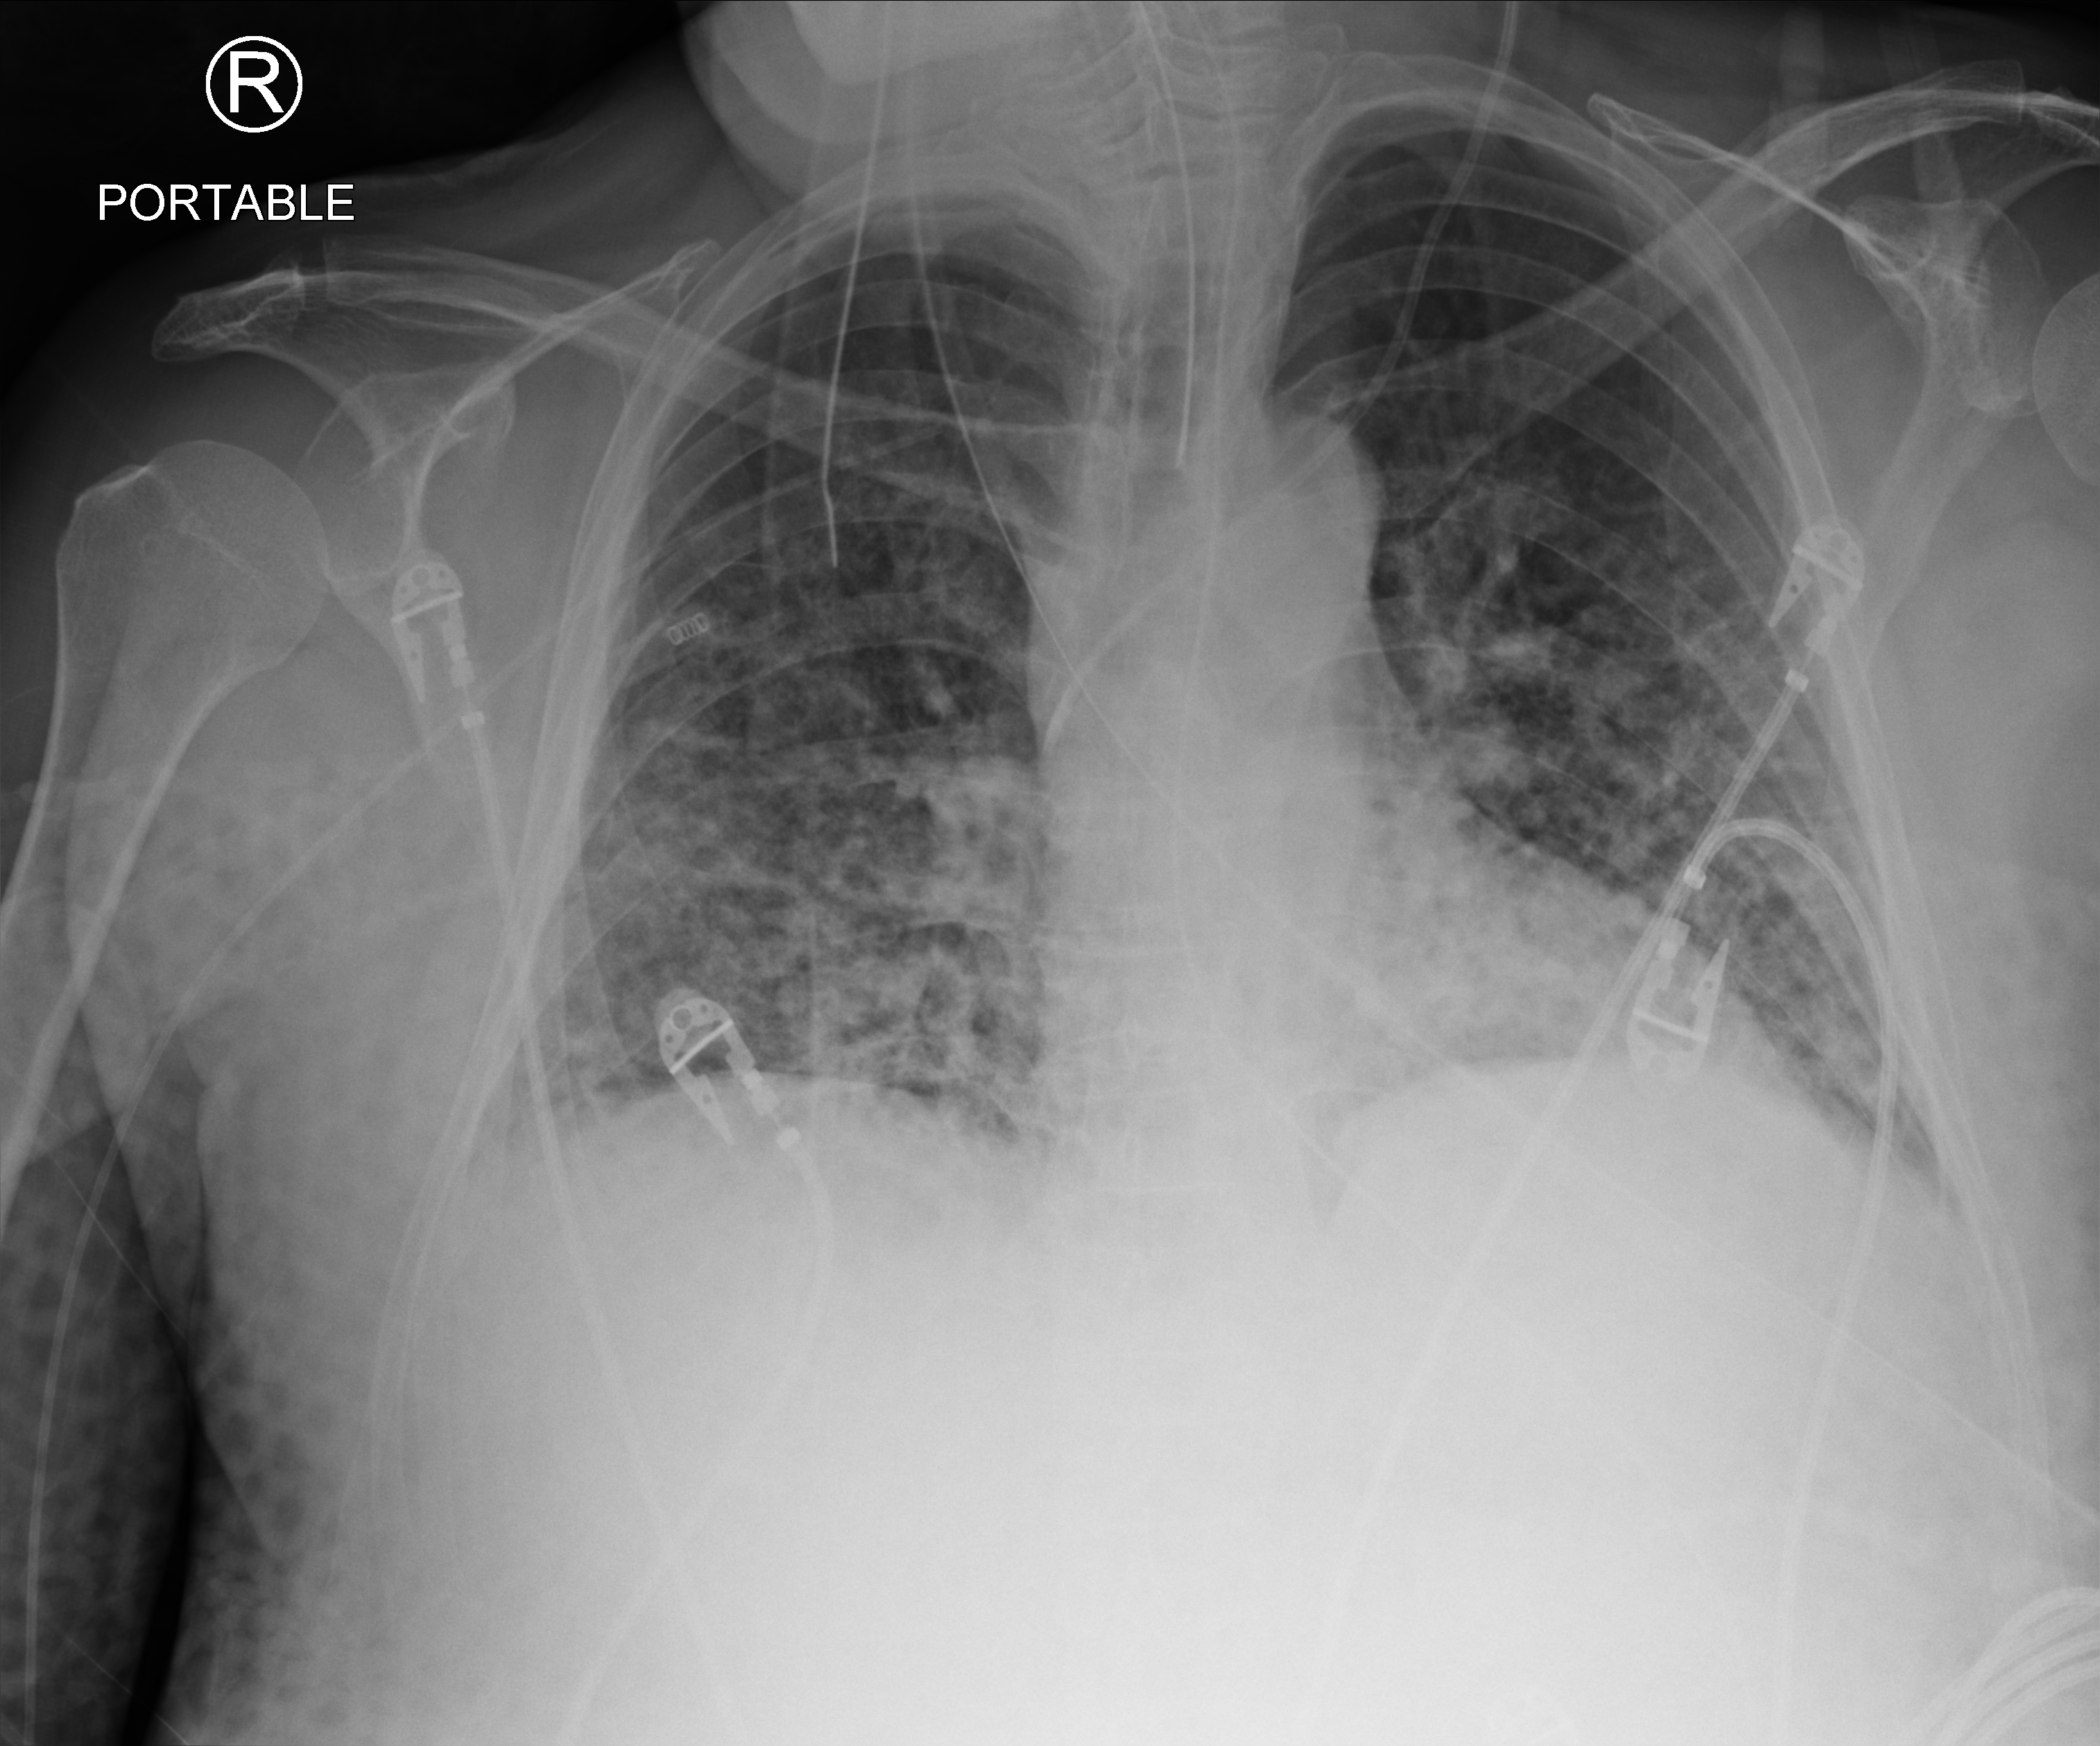
Portable chest radiograph; anteroposterior (AP) projection. Male patient hospitalised with COVID-19, age 60–74 years.
Admission-level facts for this patient (not findings on this image; timing relative to this image not recorded):
- mechanically ventilated during this hospital stay: yes